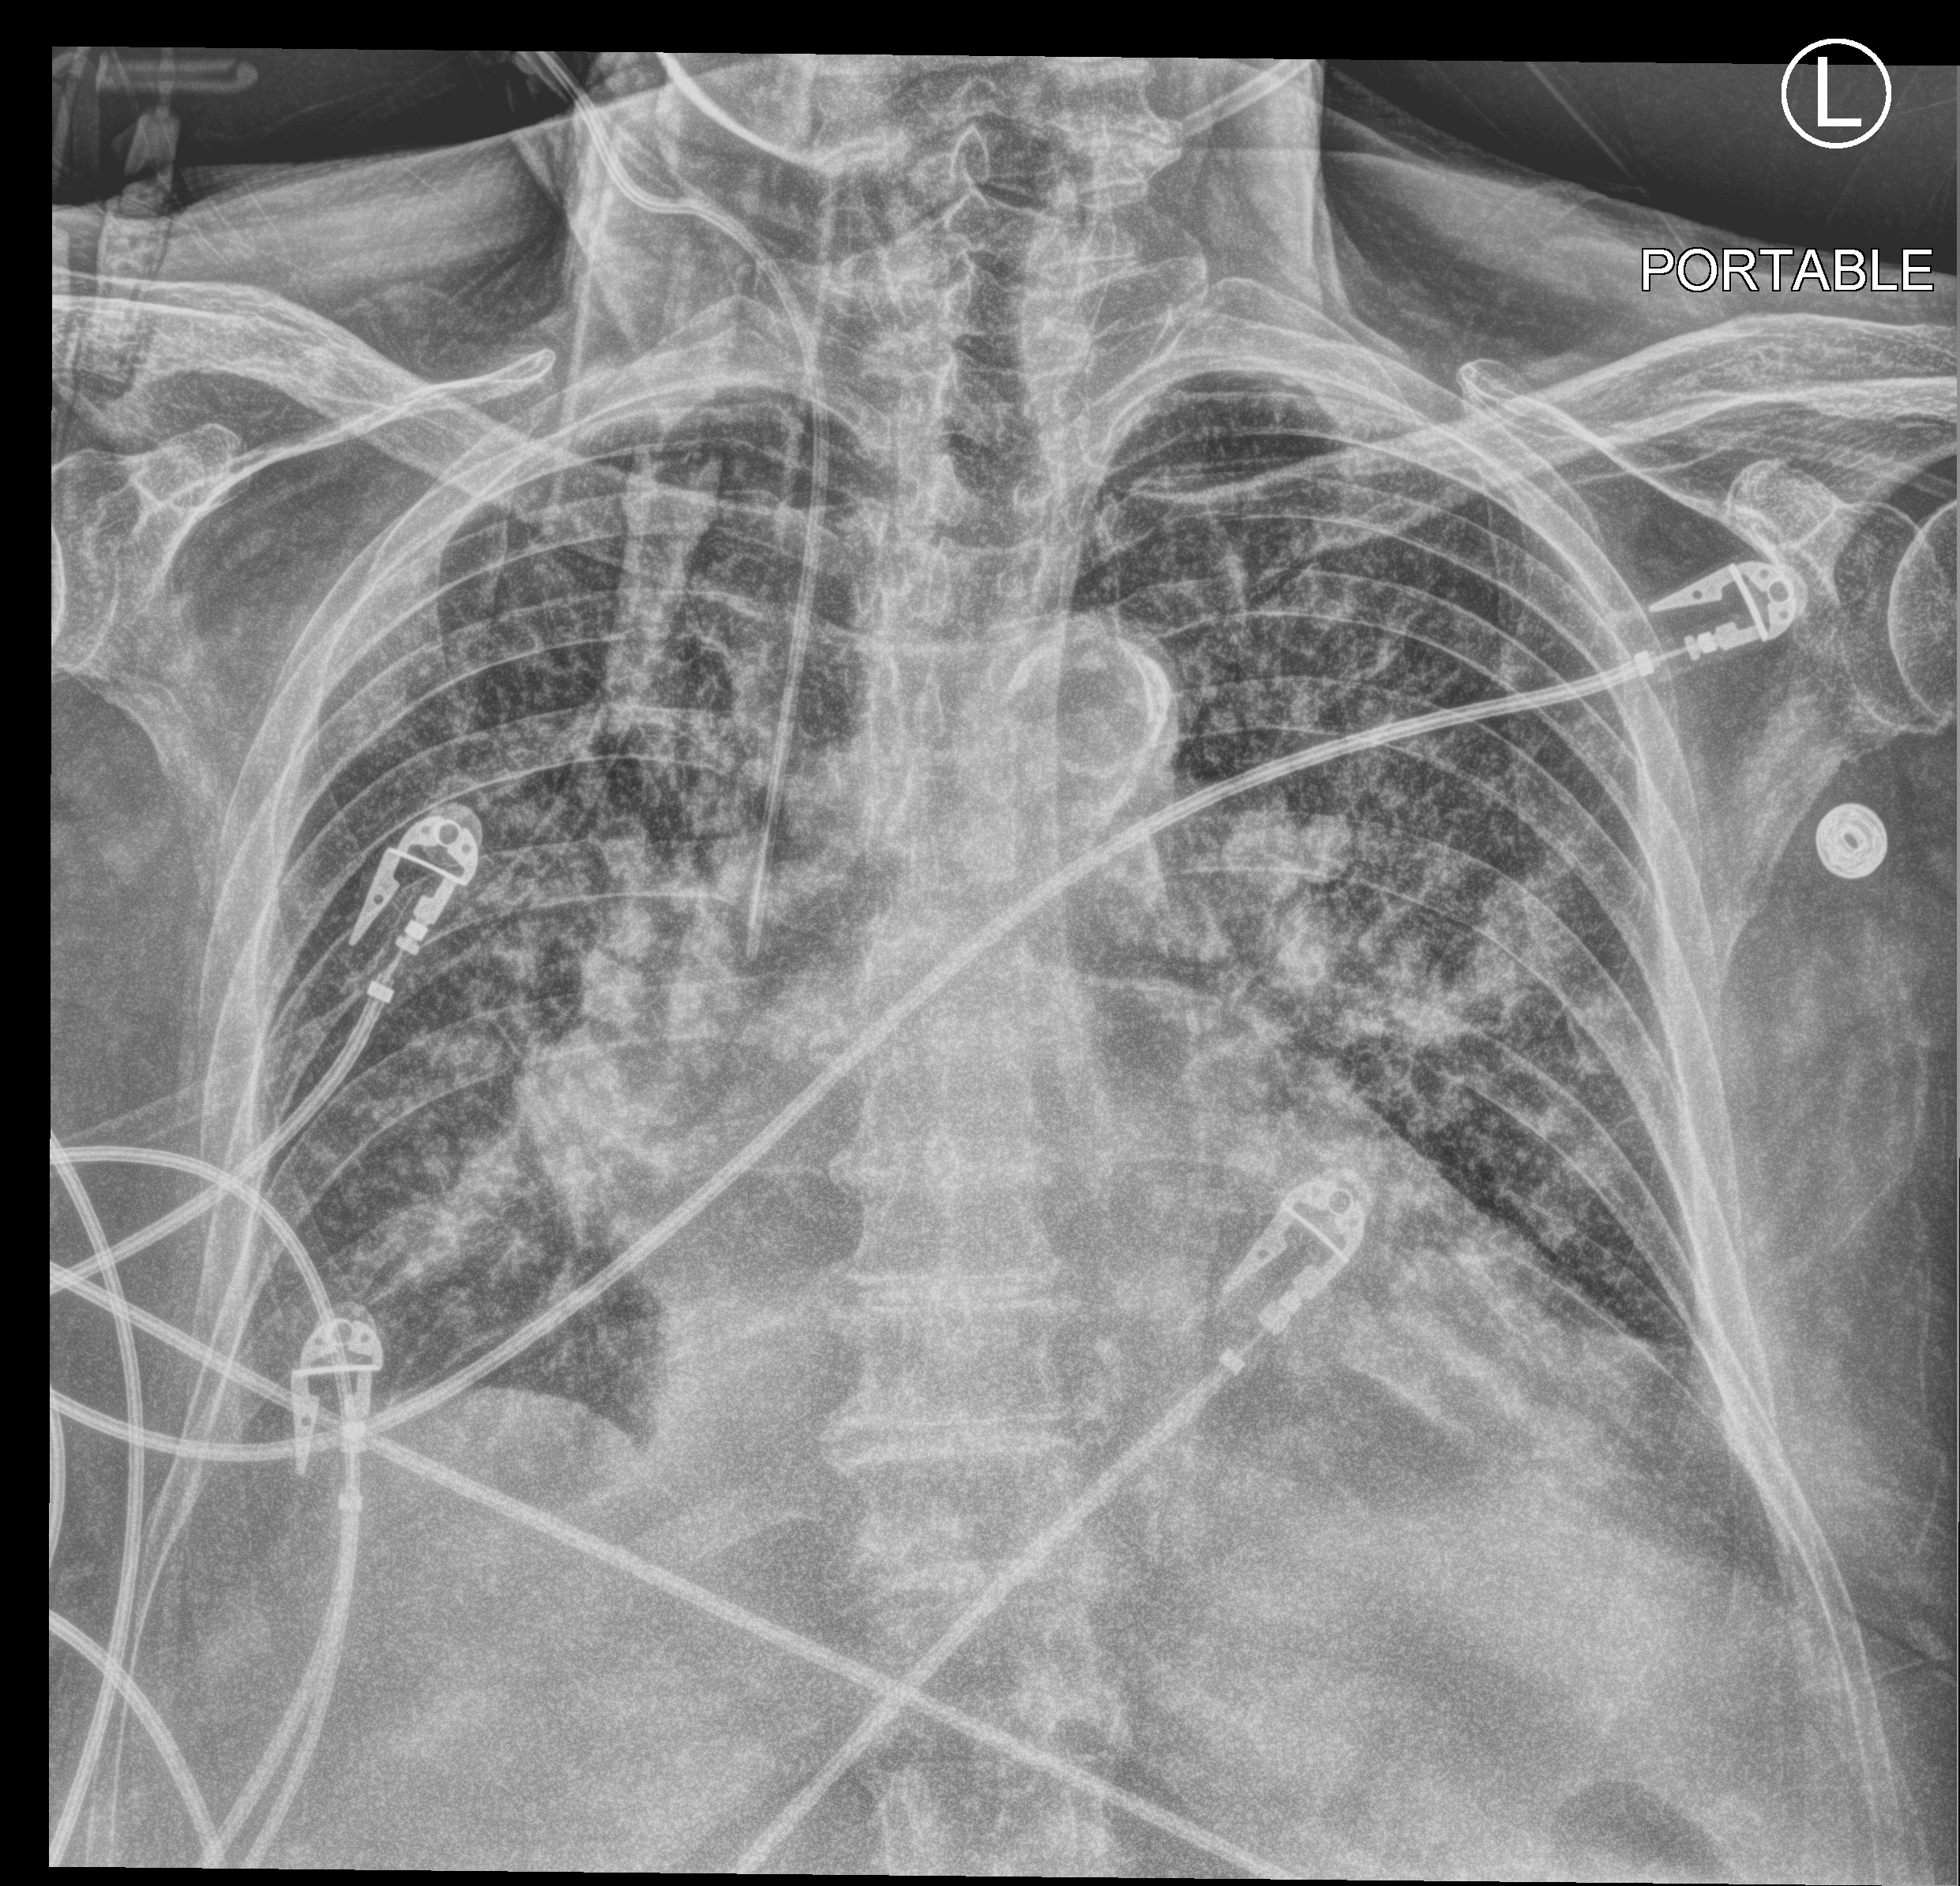
Portable chest radiograph, anteroposterior (AP) projection. Female patient hospitalised with COVID-19, age 75–90 years.
Hospital-stay facts (about this admission, not read from this image; timing relative to this image not recorded):
- mechanically ventilated during this hospital stay: no
- admitted to intensive care during this hospital stay: yes